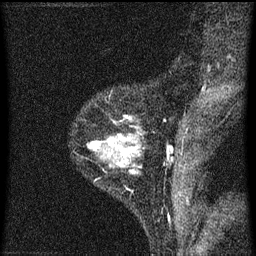
Breast MRI (dynamic contrast-enhanced), one sagittal slice. Slice 17 of 60 in the series (ordered by position). Dynamic contrast-enhanced series, image 2 of 3 at this slice position (ordered by acquisition). 1.5 T. TE 4.2 ms, TR 8 ms. 256 × 256 image matrix, field of view 180 × 180 mm. Female patient, age 33 years.
Structures marked on this image (semi-automatically segmented with operator editing):
- analysis volume of interest (the breast-tissue region the enhancement analysis was run in; not a lesion): box from (x=85, y=118) to (x=141, y=173) px
- tumour enhancement mask (voxels above the 70 % enhancement threshold inside the analysis volume of interest): (x=89, y=138)–(x=139, y=171)